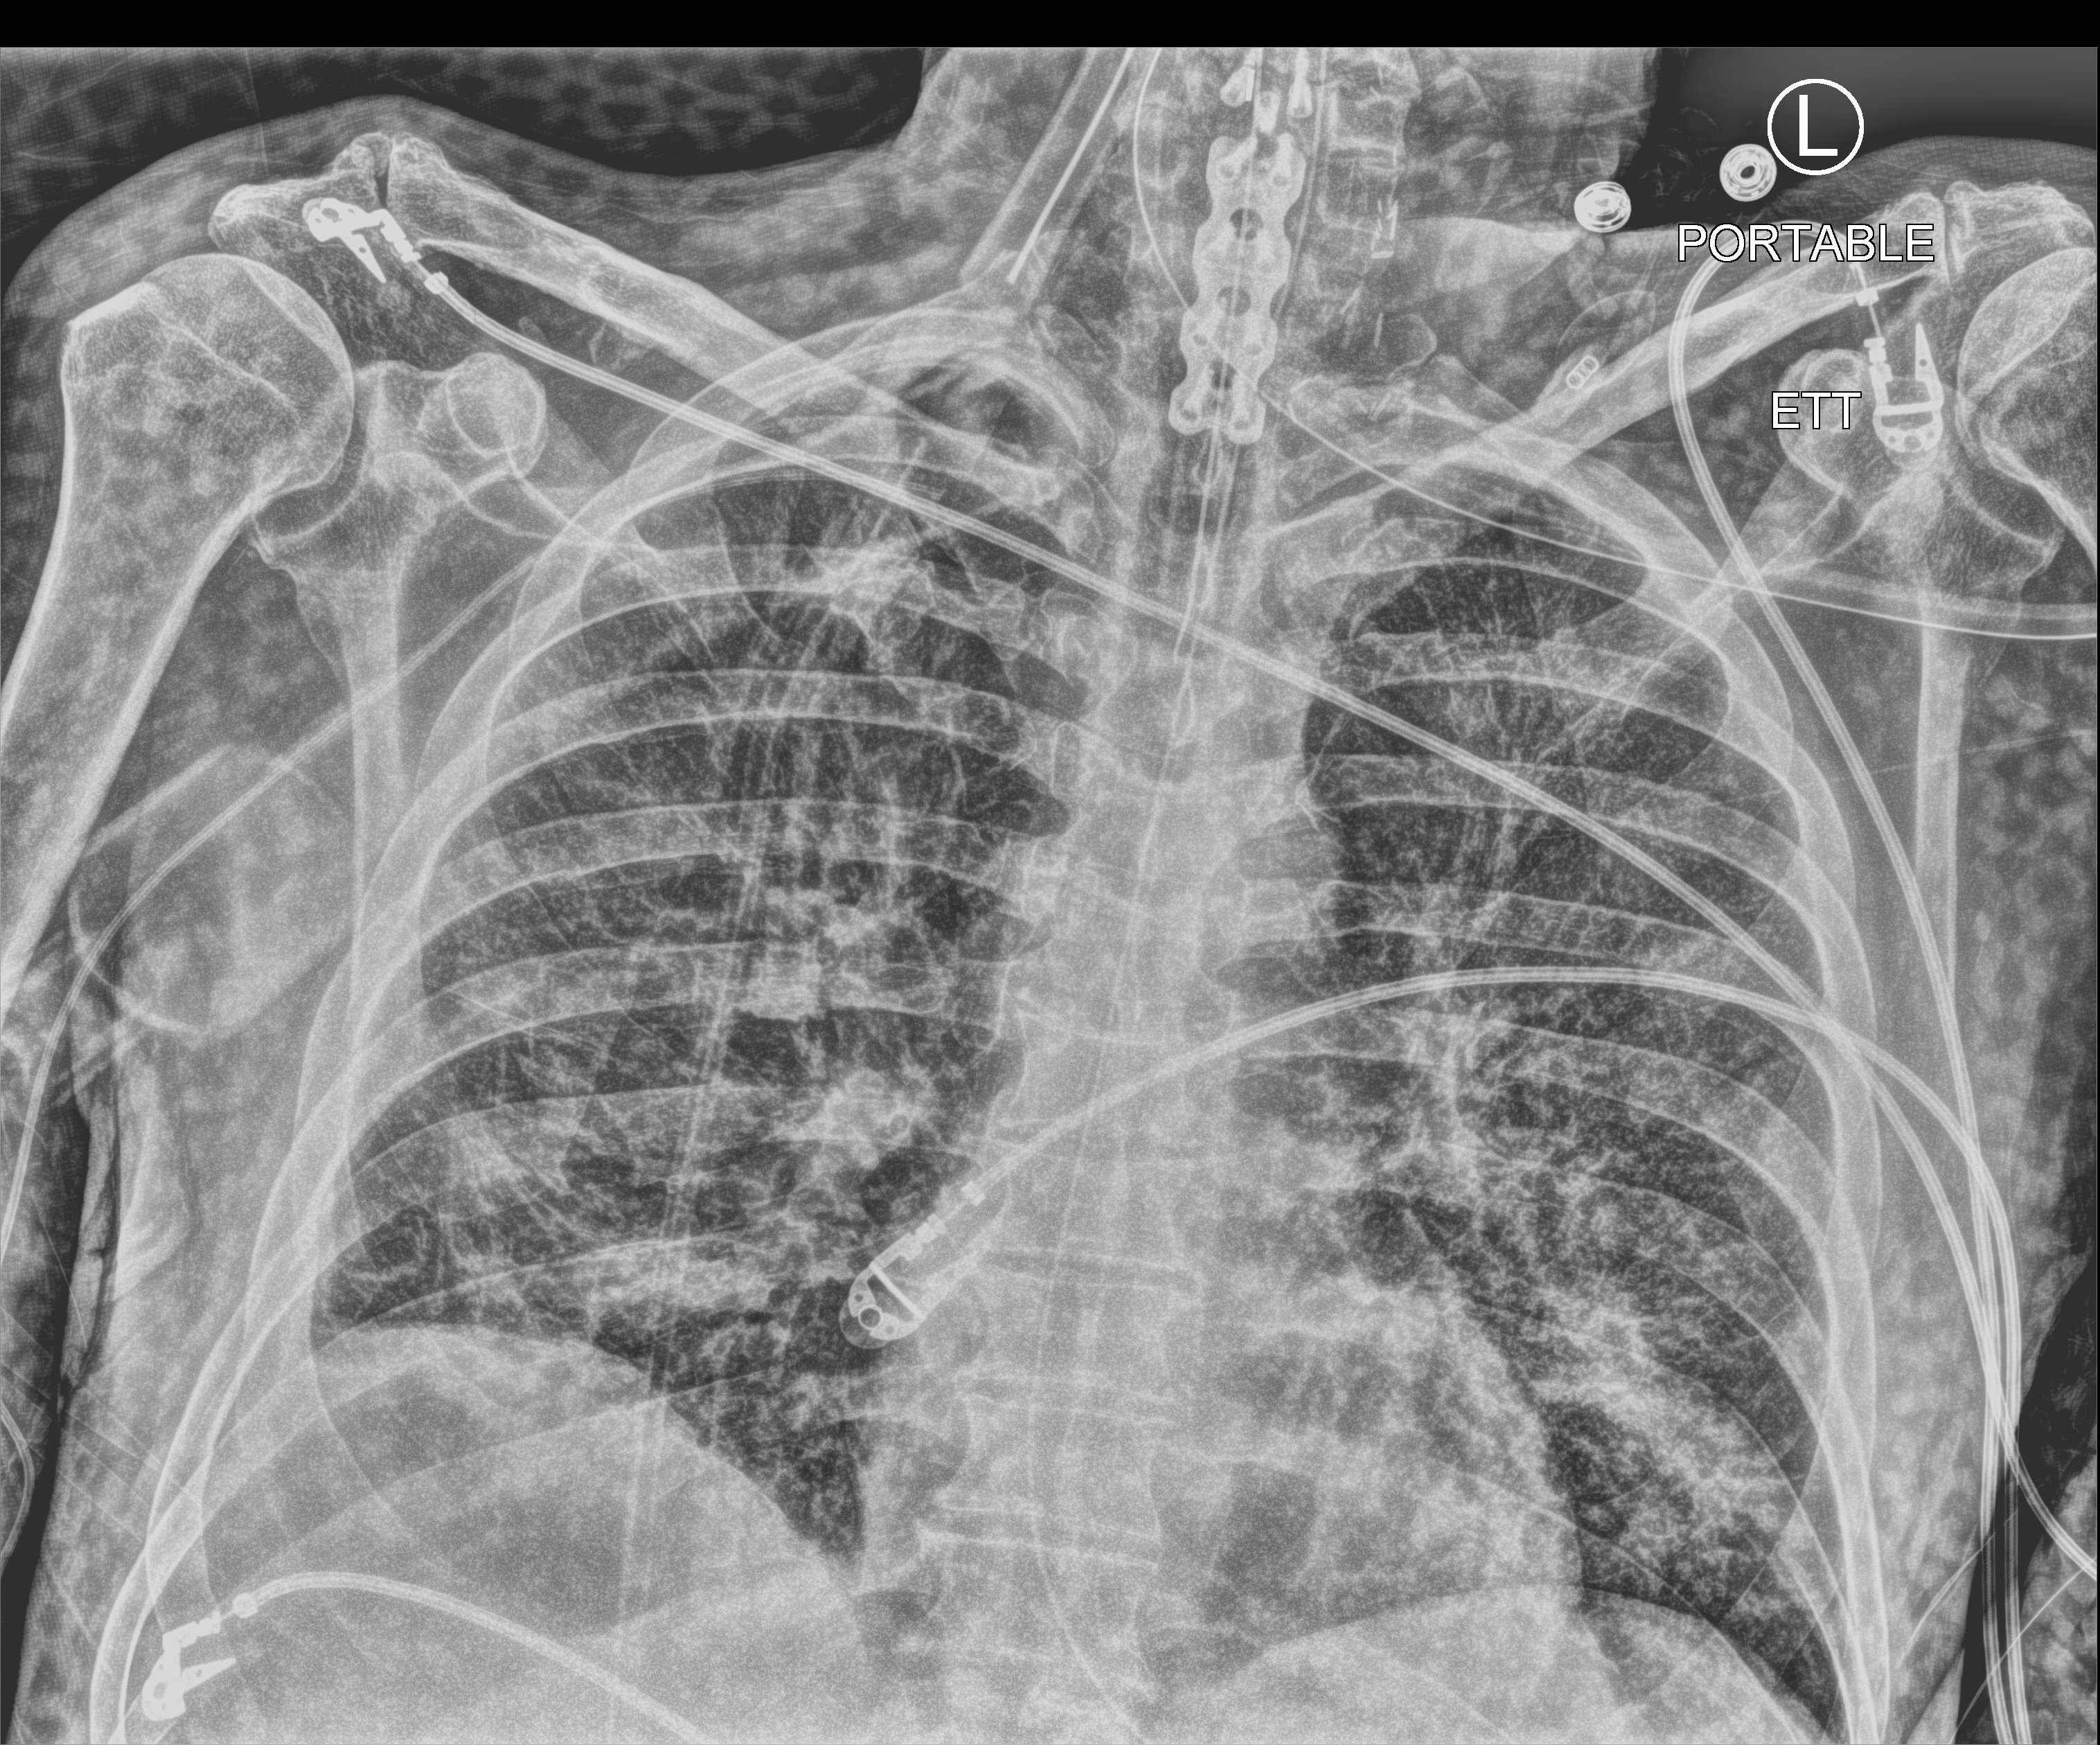
Bedside chest radiograph (computed radiography), anteroposterior (AP) projection. Patient hospitalised with COVID-19; male, aged 60–74 years.
Hospital-stay facts (about this admission, not read from this image; timing relative to this image not recorded): length of hospital stay: 43 days.